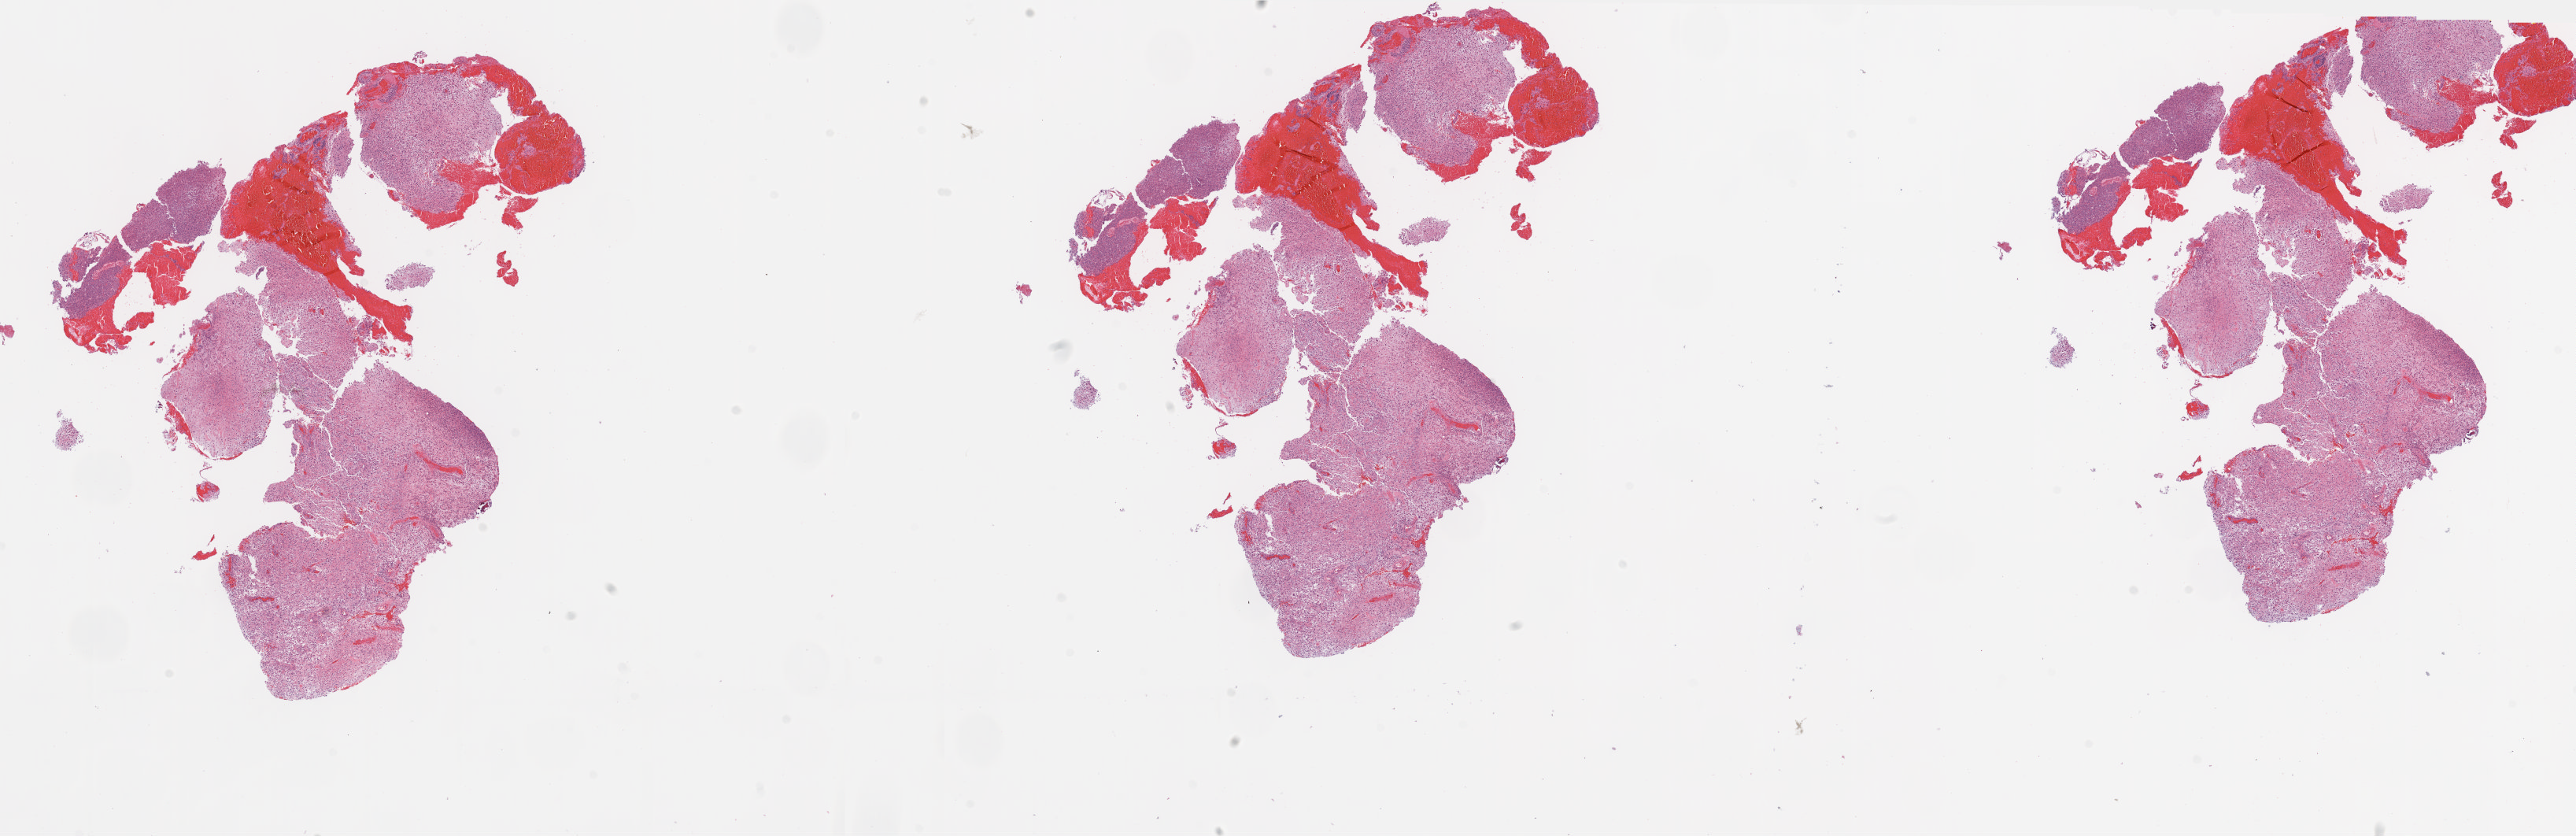
H&E whole-slide image — shown as a low-resolution overview of the whole scanned area (about 26.2 x 8.5 mm, acquisition: 5x scan). Frozen section from the top of the tissue portion. Sample: primary tumour, brain. Patient: female, age at initial diagnosis 72 years. Pathologist review of this section (percent, as recorded): tumour cells 87%, tumour nuclei 80%, normal cells 0%, stromal cells 5%, necrosis 8%.
• diagnosis: Glioblastoma